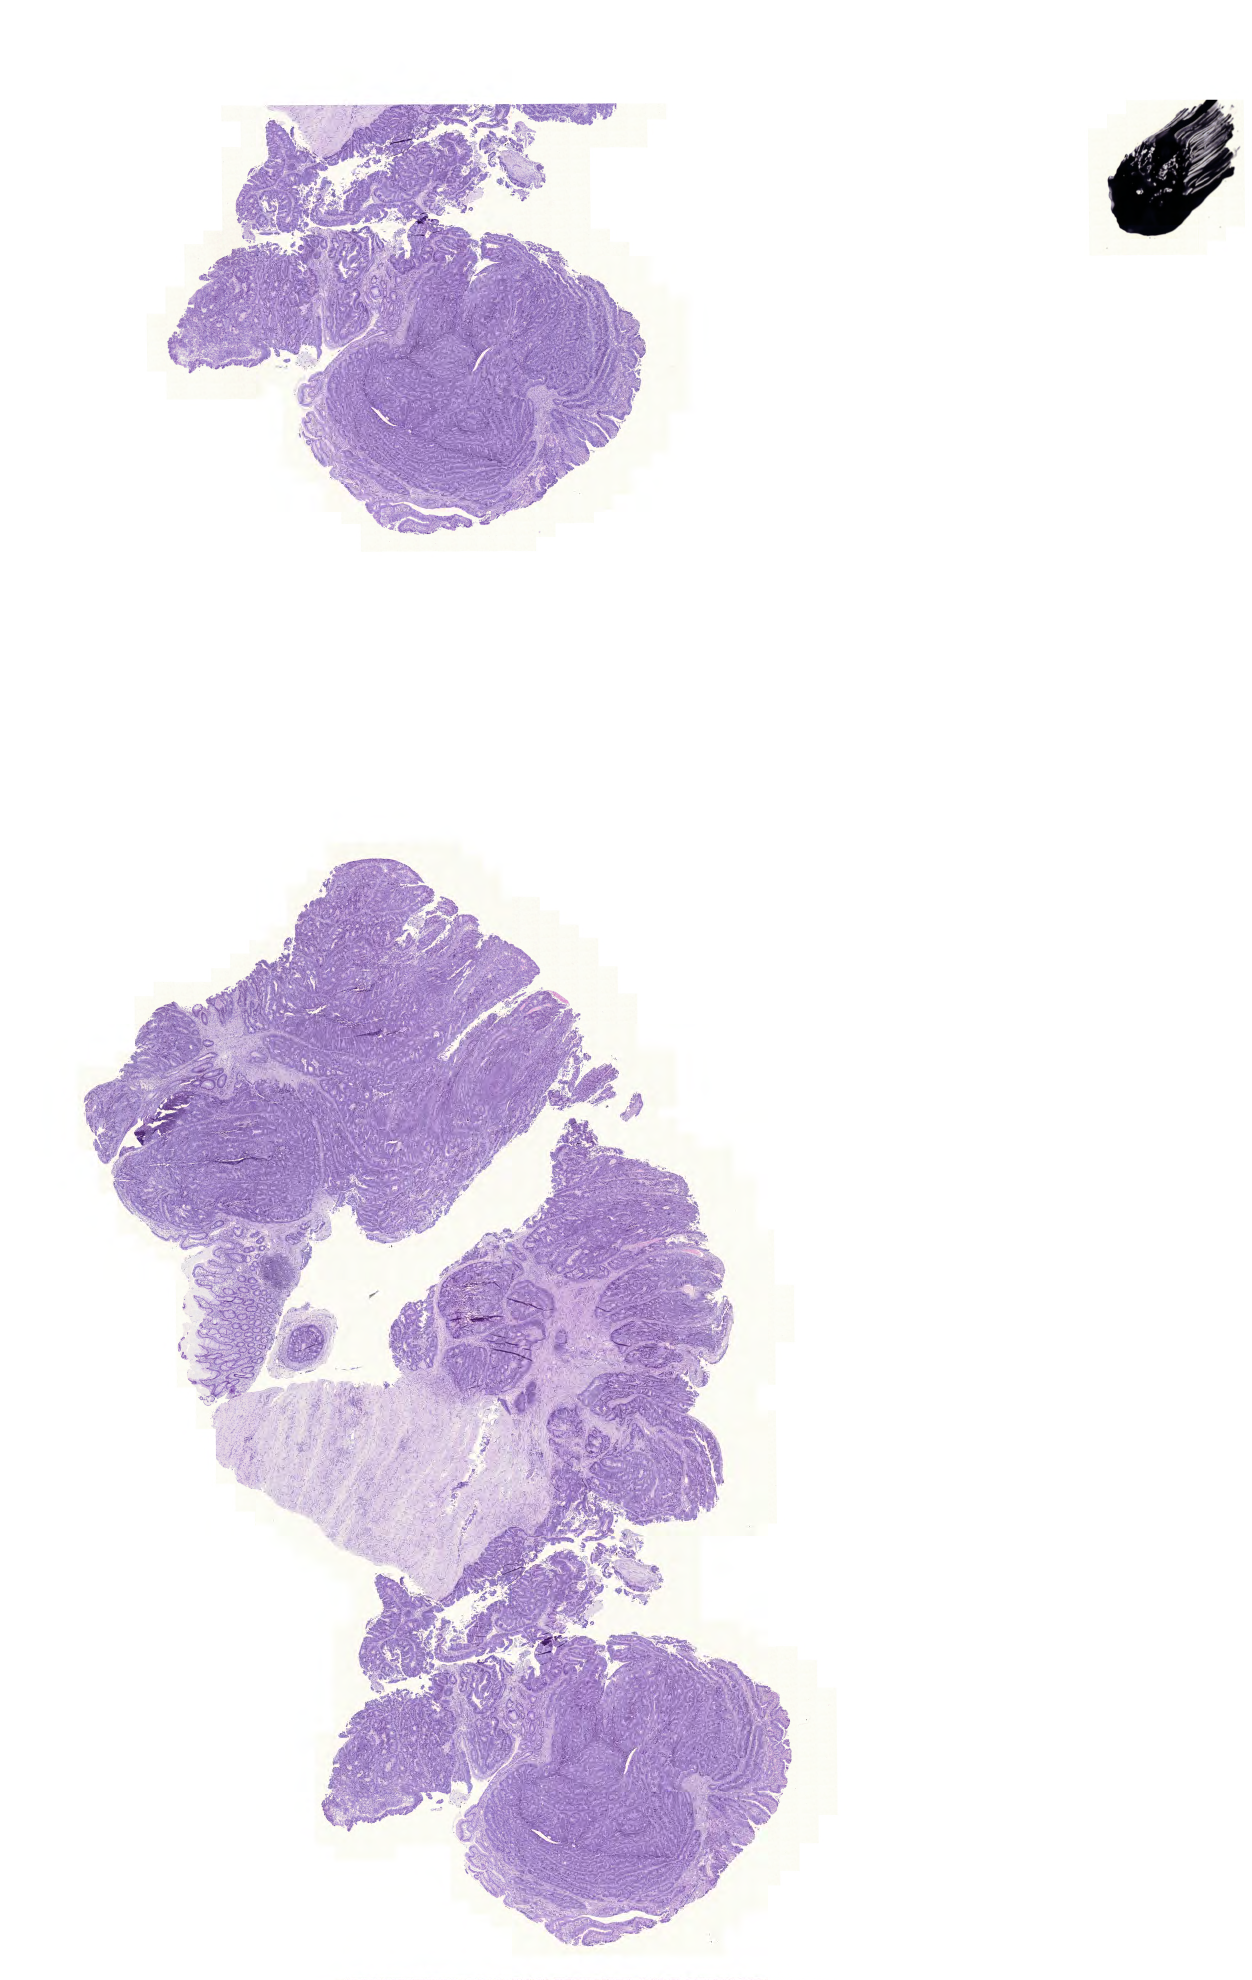
Digitized Hematoxylin and eosin (H&E) stained tissue section (whole slide), whole scanned area (about 18.6 x 29.5 mm, slide scanned at 20x) shown as a low-resolution overview; formalin-fixed paraffin-embedded (FFPE) diagnostic section; sample: primary tumour, colon. Patient: female, age at initial diagnosis 75 years.
AJCC pathologic stage: IIA (6th edition). Diagnosis: Adenocarcinoma, NOS.